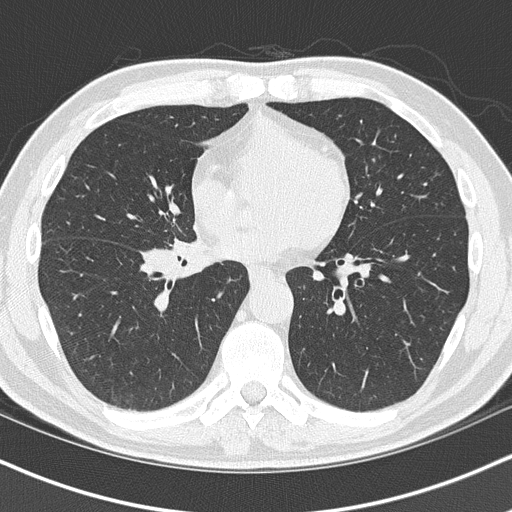
Low-dose screening chest CT, axial slice, baseline annual screen, lung window (W 1500 / L -600 HU), 2 mm slice thickness, lung (sharp) reconstruction kernel (B50f), slice 56 of 151 in the series. Male, age 55 years at enrolment.
• Expert-annotated lung lesion, bounding box <134,226,239,305> (left, top, right, bottom; pixels).
• Reader record for this screening exam (exam-level; its link to the box is not recorded): non-calcified nodule or mass ≥4 mm, right lower lobe, 6 × 5 mm, spiculated (stellate) margins, soft tissue attenuation.
• Later outcome: lung cancer diagnosed 21 days after this screen — carcinoma, NOS, right hilum, stage IB (AJCC 6th edition), 67 mm at pathology.